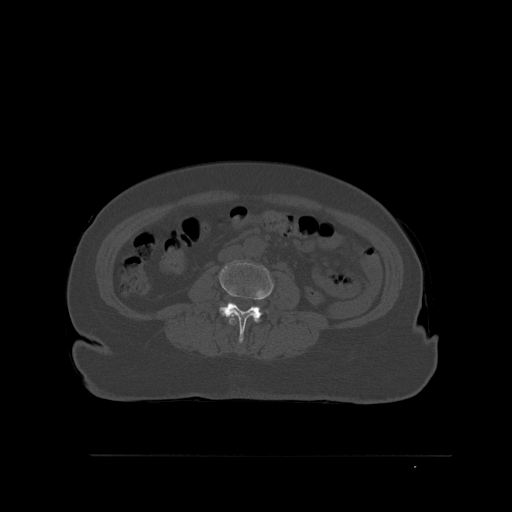
CT including the spine, one axial slice; slice 224 of 527 in the series (ordered by position); bone window (W 1800 / L 400 HU); 1.5 mm slice thickness; 512 × 512 image matrix, field of view 470 × 470 mm. Female patient, age 73 years. From the clinical record (not read from this slice): primary cancer: breast; vertebrae with lytic lesions (as recorded): L2.
Outlined on this slice (semi-automatic segmentation, software-assisted and operator-edited):
- L2 vertebra: box from (x=229, y=313) to (x=237, y=325) px
- L3 vertebra: (x=219, y=260)–(x=274, y=343)